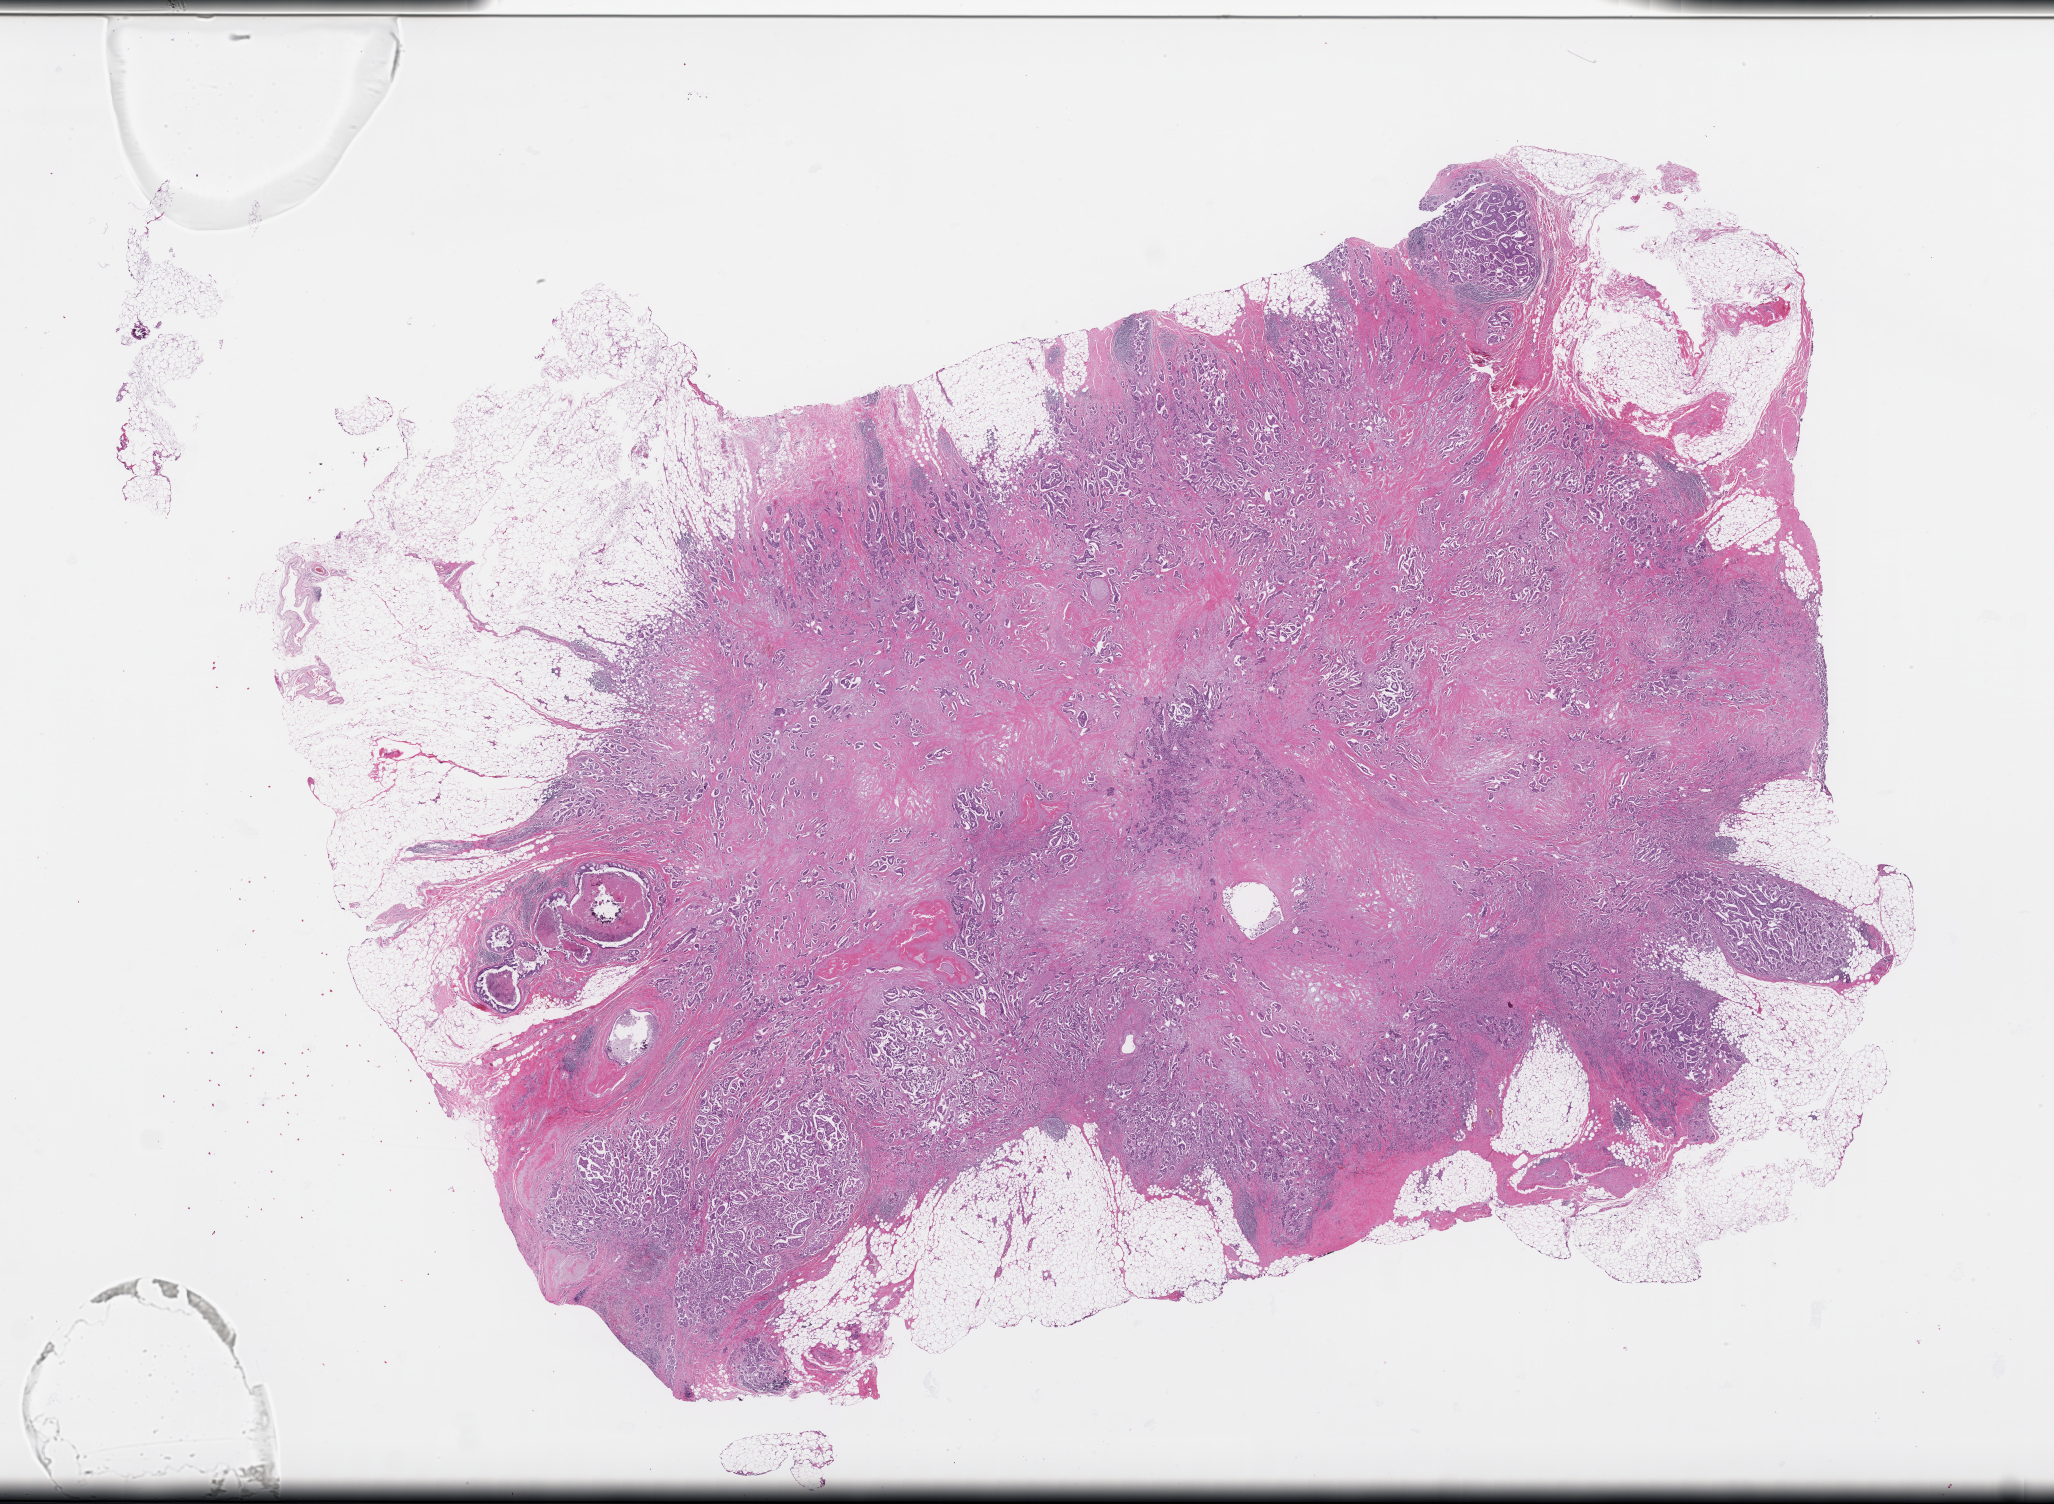
Whole-slide image, hematoxylin and eosin (H&E) stain — low-resolution overview of the scanned area, about 33.2 x 24.3 mm. FFPE section. Tissue site: breast. Specimen time point: archival tissue. Patient sex: female.
This section: primary tumour tissue. Diagnosis: Invasive Breast Carcinoma.